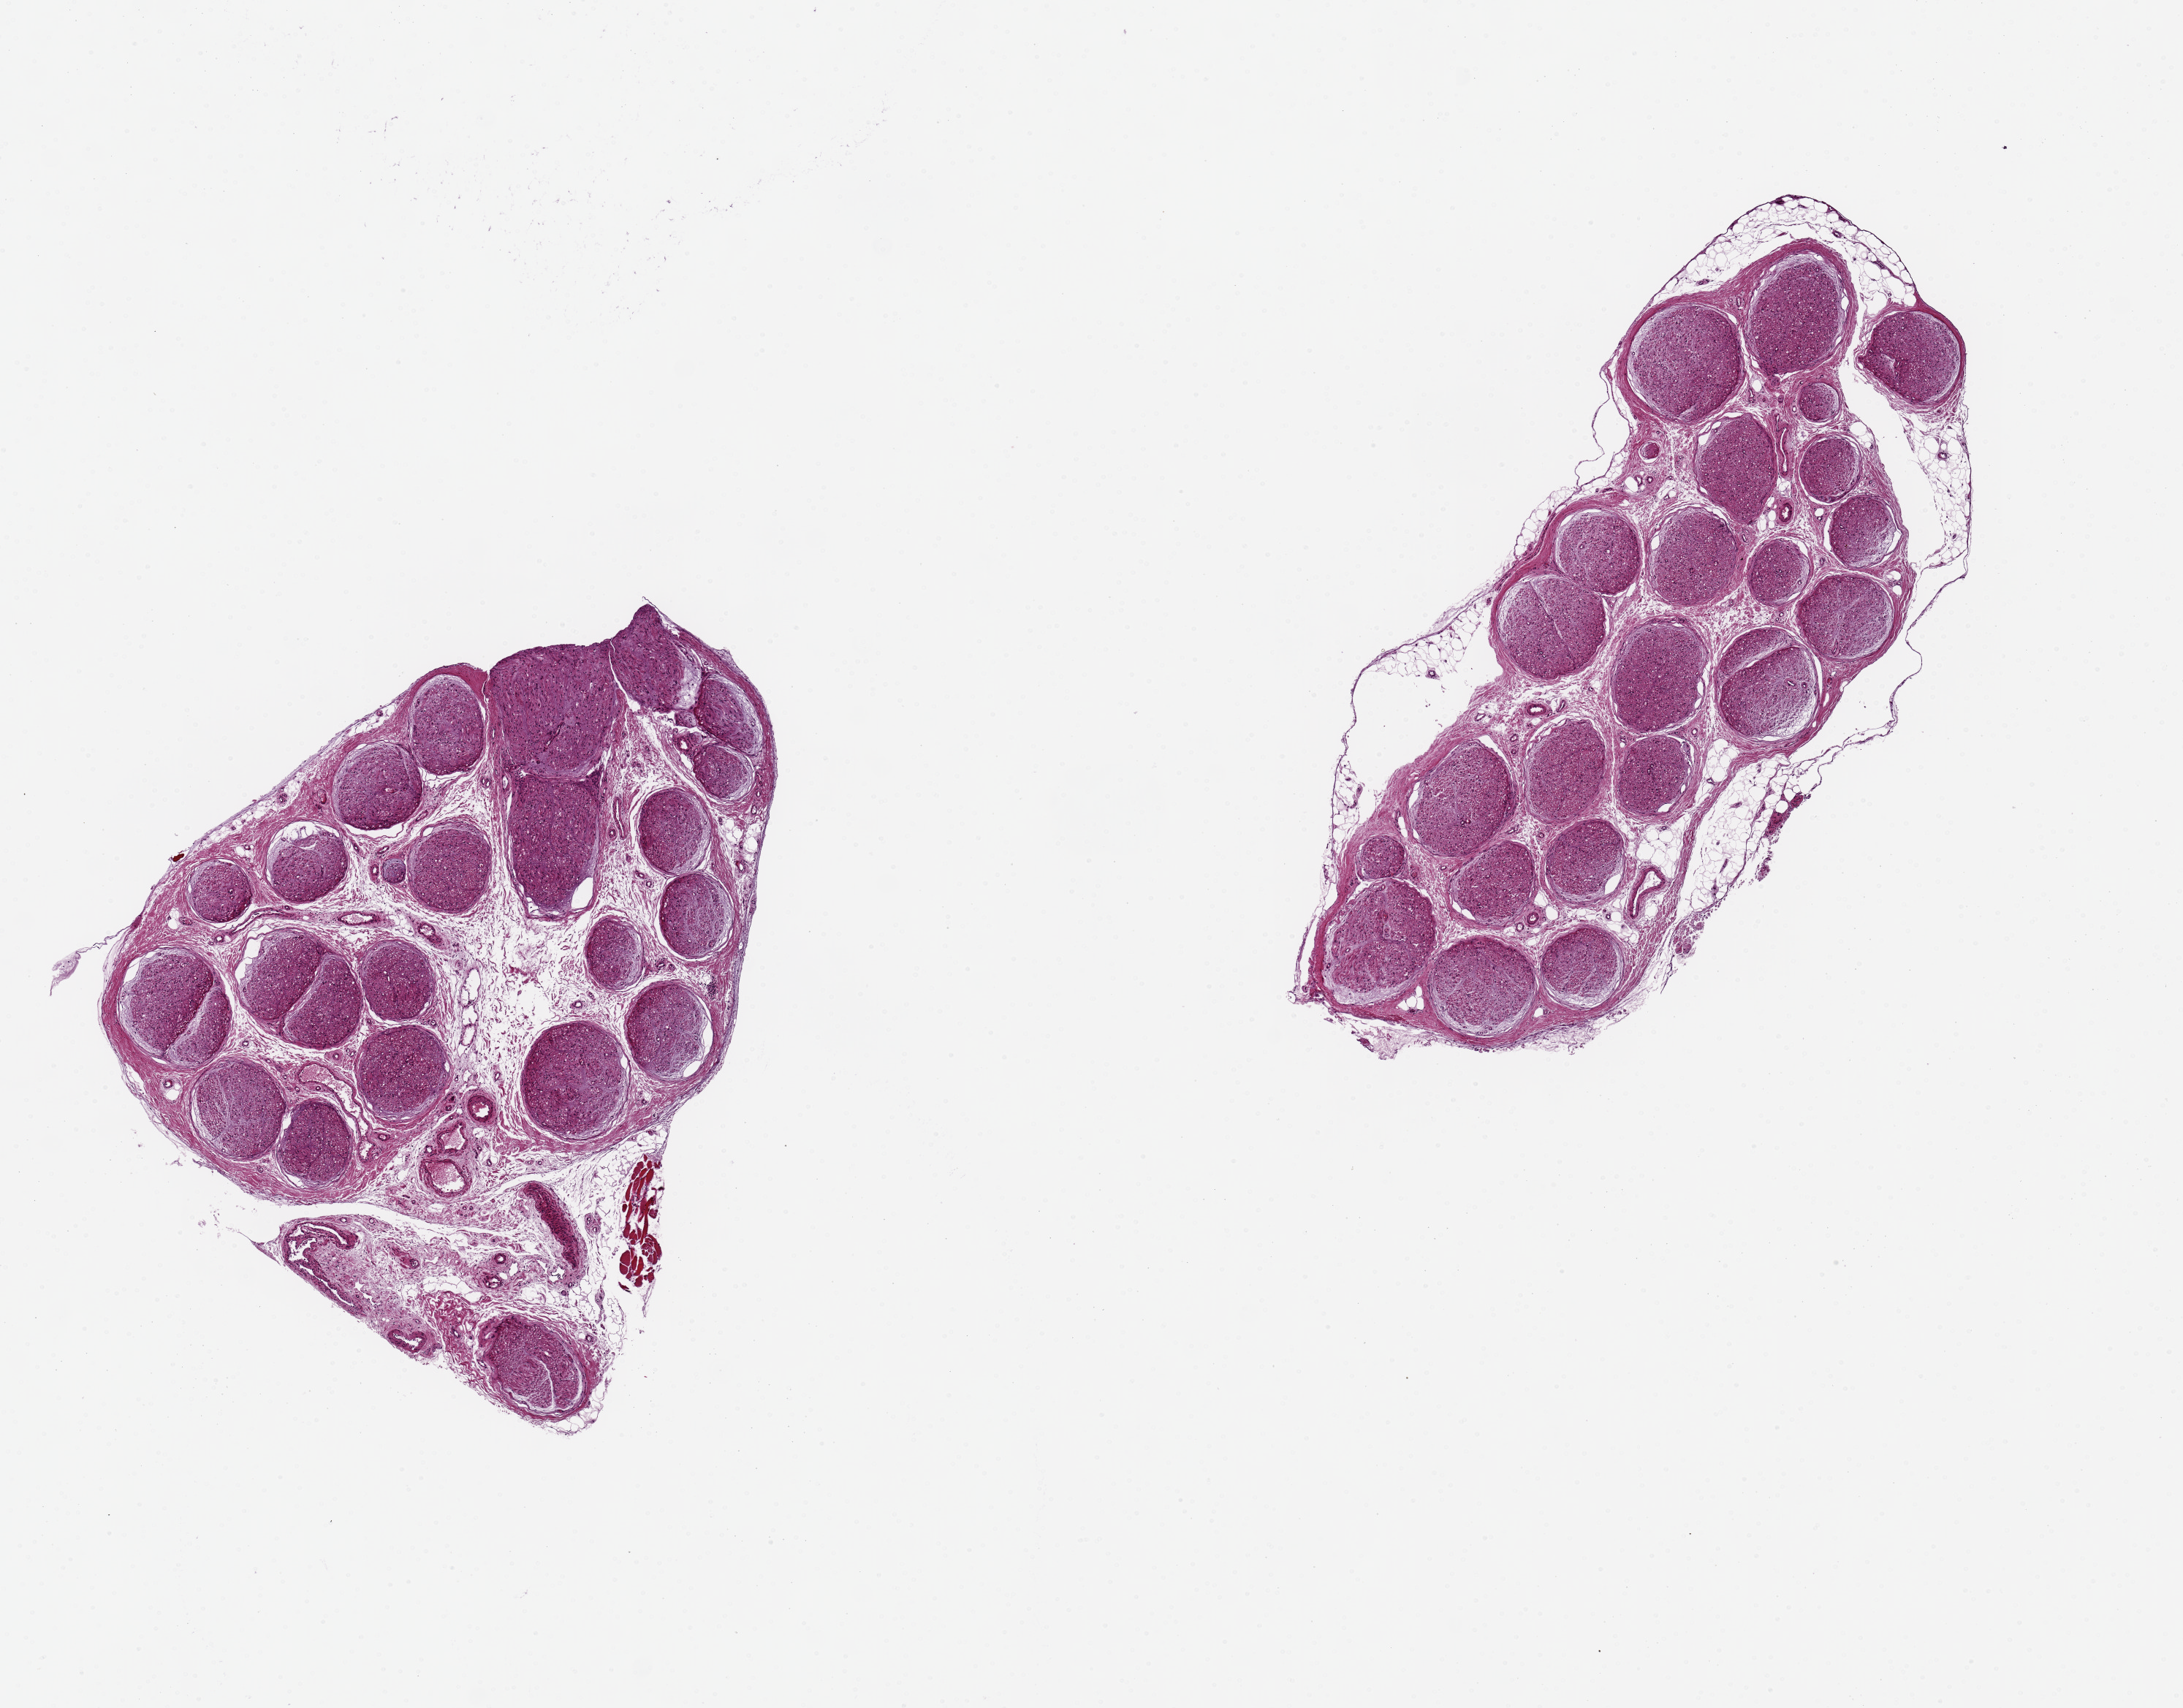
Hematoxylin and eosin (H&E) whole-slide image — shown as a low-resolution overview of the whole scanned area (about 11.8 x 9.2 mm), PAXgene-fixed, paraffin-embedded tissue, target tissue: tibial nerve, donor tissue sample. Female donor.
- pathologist's review note for this sample: 2 pieces 3.8x3.5 & 5x1.8 mm